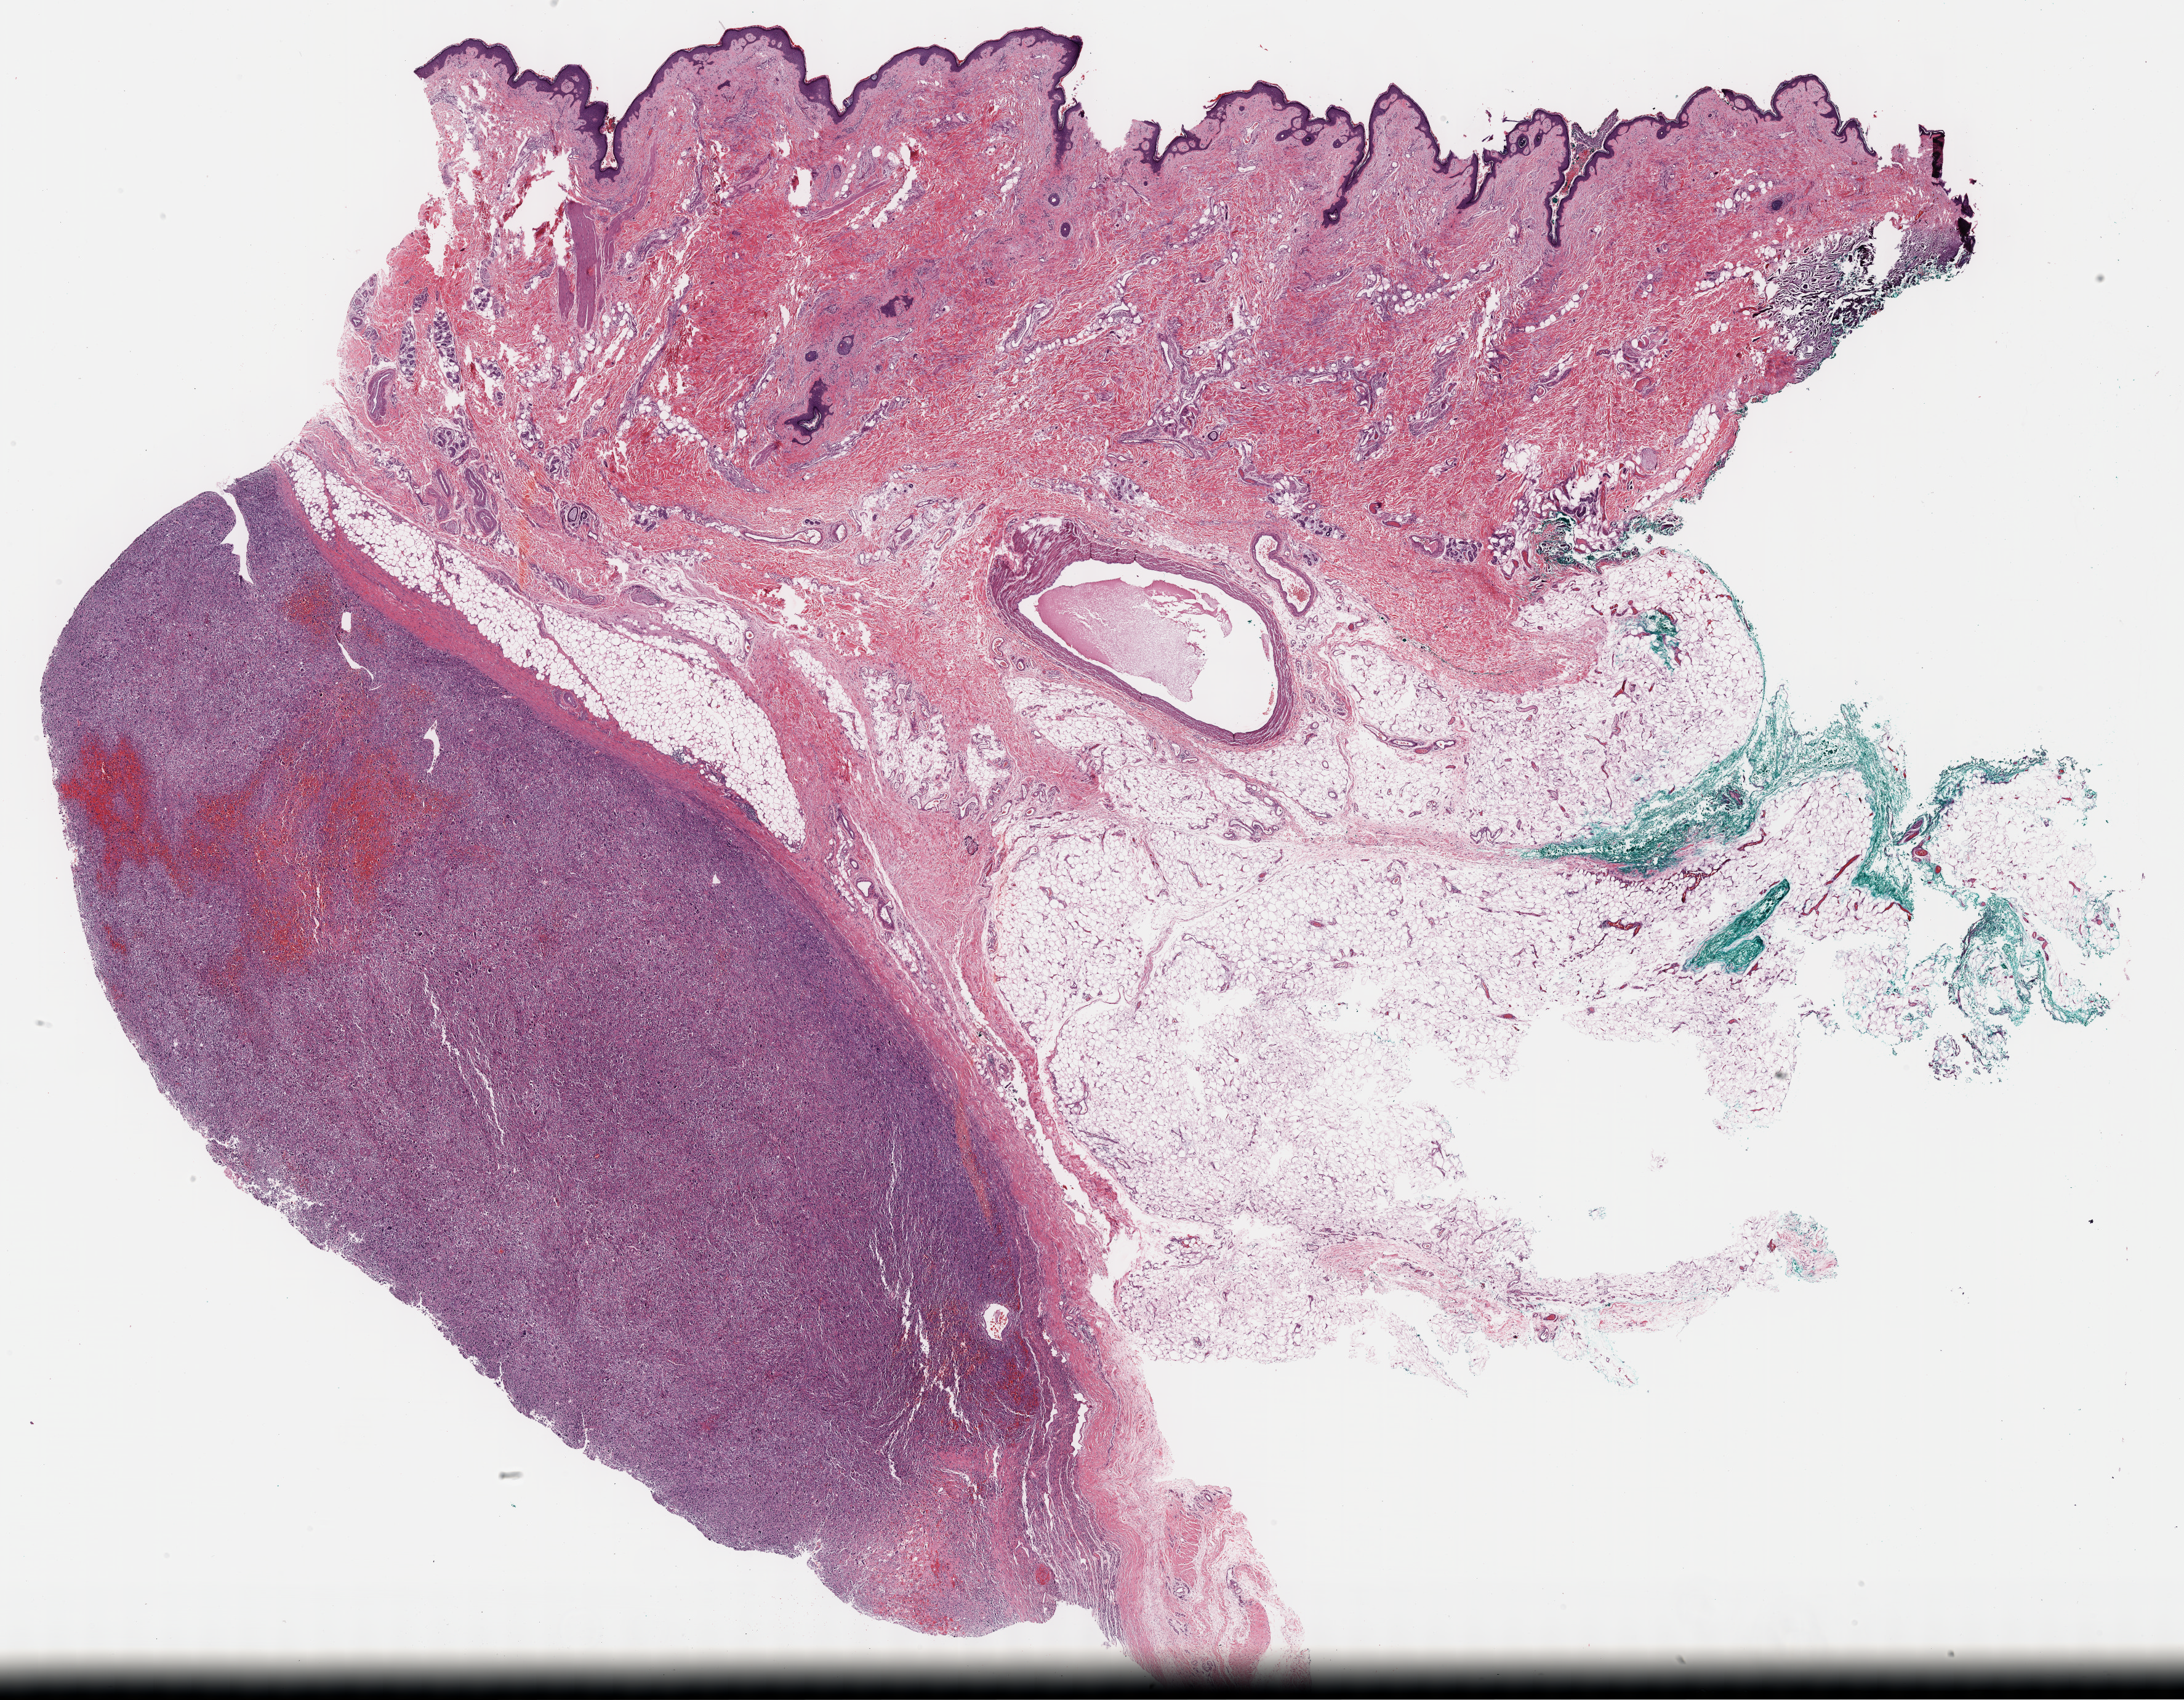
Whole-slide histology image, Hematoxylin and eosin (H&E) stained — low-resolution overview of the scanned area, about 28.7 x 22.3 mm, FFPE section, sample: primary tumour, connective, subcutaneous and other soft tissues. Female patient; age at initial diagnosis 78 years.
Diagnosis: Malignant fibrous histiocytoma (connective, subcutaneous and other soft tissues of lower limb and hip).